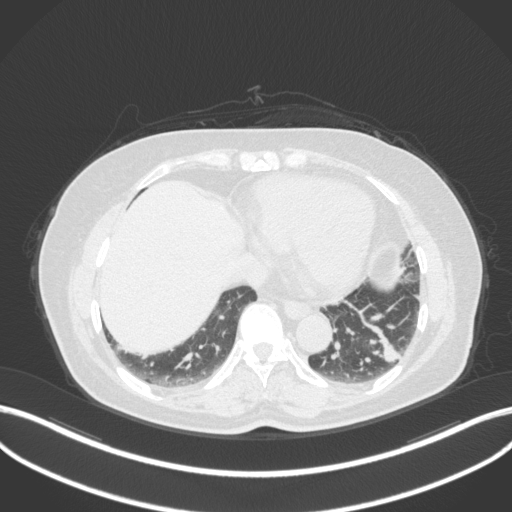
Chest CT, one axial slice; position 115 of 307 along the scan axis; 120 kVp; lung window (W 1500 / L -600 HU); 512 × 512 image matrix, field of view 400 × 400 mm. Patient: female, 59 years. Case-level facts recorded for this patient, not image findings: clinical TNM (as recorded): T2a N0 M0; histopathological grade: G2-3.
Outlined on this slice (rectangle marked by the reading radiologist):
- lung tumour (recorded histology: adenocarcinoma): bounding box [x1, y1, x2, y2] px = [357, 309, 401, 365]